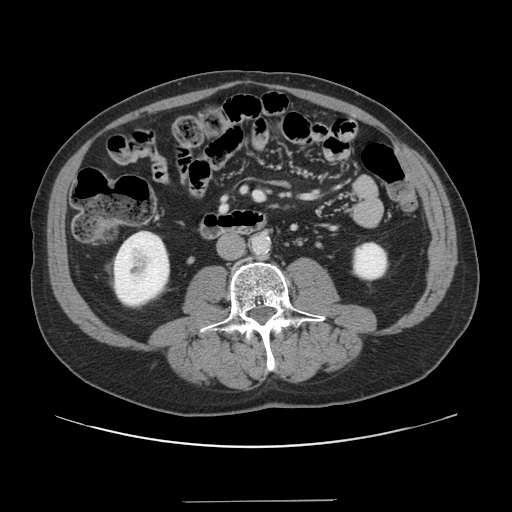
Contrast-enhanced abdominal CT, one axial slice. 120 kVp. Intravenous contrast given. Soft-tissue window (W 400 / L 40 HU). 2.5 mm slice thickness. 512 × 512 image matrix, field of view 399 × 399 mm. Male patient, age 63 years. Case-level facts recorded for this patient, not image findings: diagnosis: colorectal cancer liver metastases, imaged before liver resection; multiple liver metastases: no.
Outlined on this slice (manually delineated by an expert):
- portal vein (with intrahepatic branches): bounding box (x1, y1, x2, y2) in pixels: (254, 192, 262, 199)